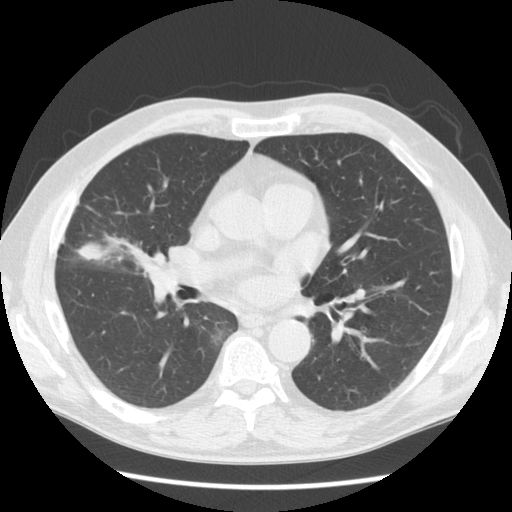
Low-dose screening chest CT, one axial slice; slice 79 of 146 in the series (ordered by position); 120 kVp; lung window (W 1500 / L -600 HU); 2.5 mm slice thickness; 512 × 512 image matrix, field of view 350 × 350 mm.
Structures marked on this image (manually delineated by an expert):
- lesion 1 (tumor, middle lobe of right lung): bounding box [x1, y1, x2, y2] px = [79, 246, 105, 259]